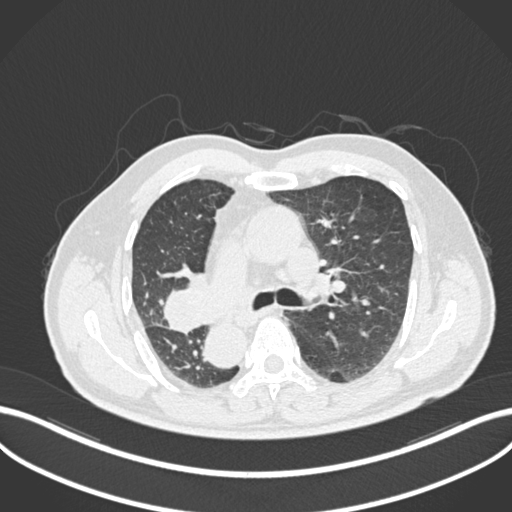
Chest CT, one axial slice; slice 147 of 206 in the series (ordered by position); 120 kVp; lung window (W 1500 / L -600 HU); 512 × 512 image matrix, field of view 400 × 400 mm. Patient: male, 67 years. Case-level facts recorded for this patient, not image findings: clinical TNM (as recorded): T2a N0 M0.
Outlined on this slice (rectangle marked by the reading radiologist):
- lung tumour (recorded histology: squamous cell carcinoma): bounding box (x1, y1, x2, y2) in pixels: (159, 268, 208, 336)